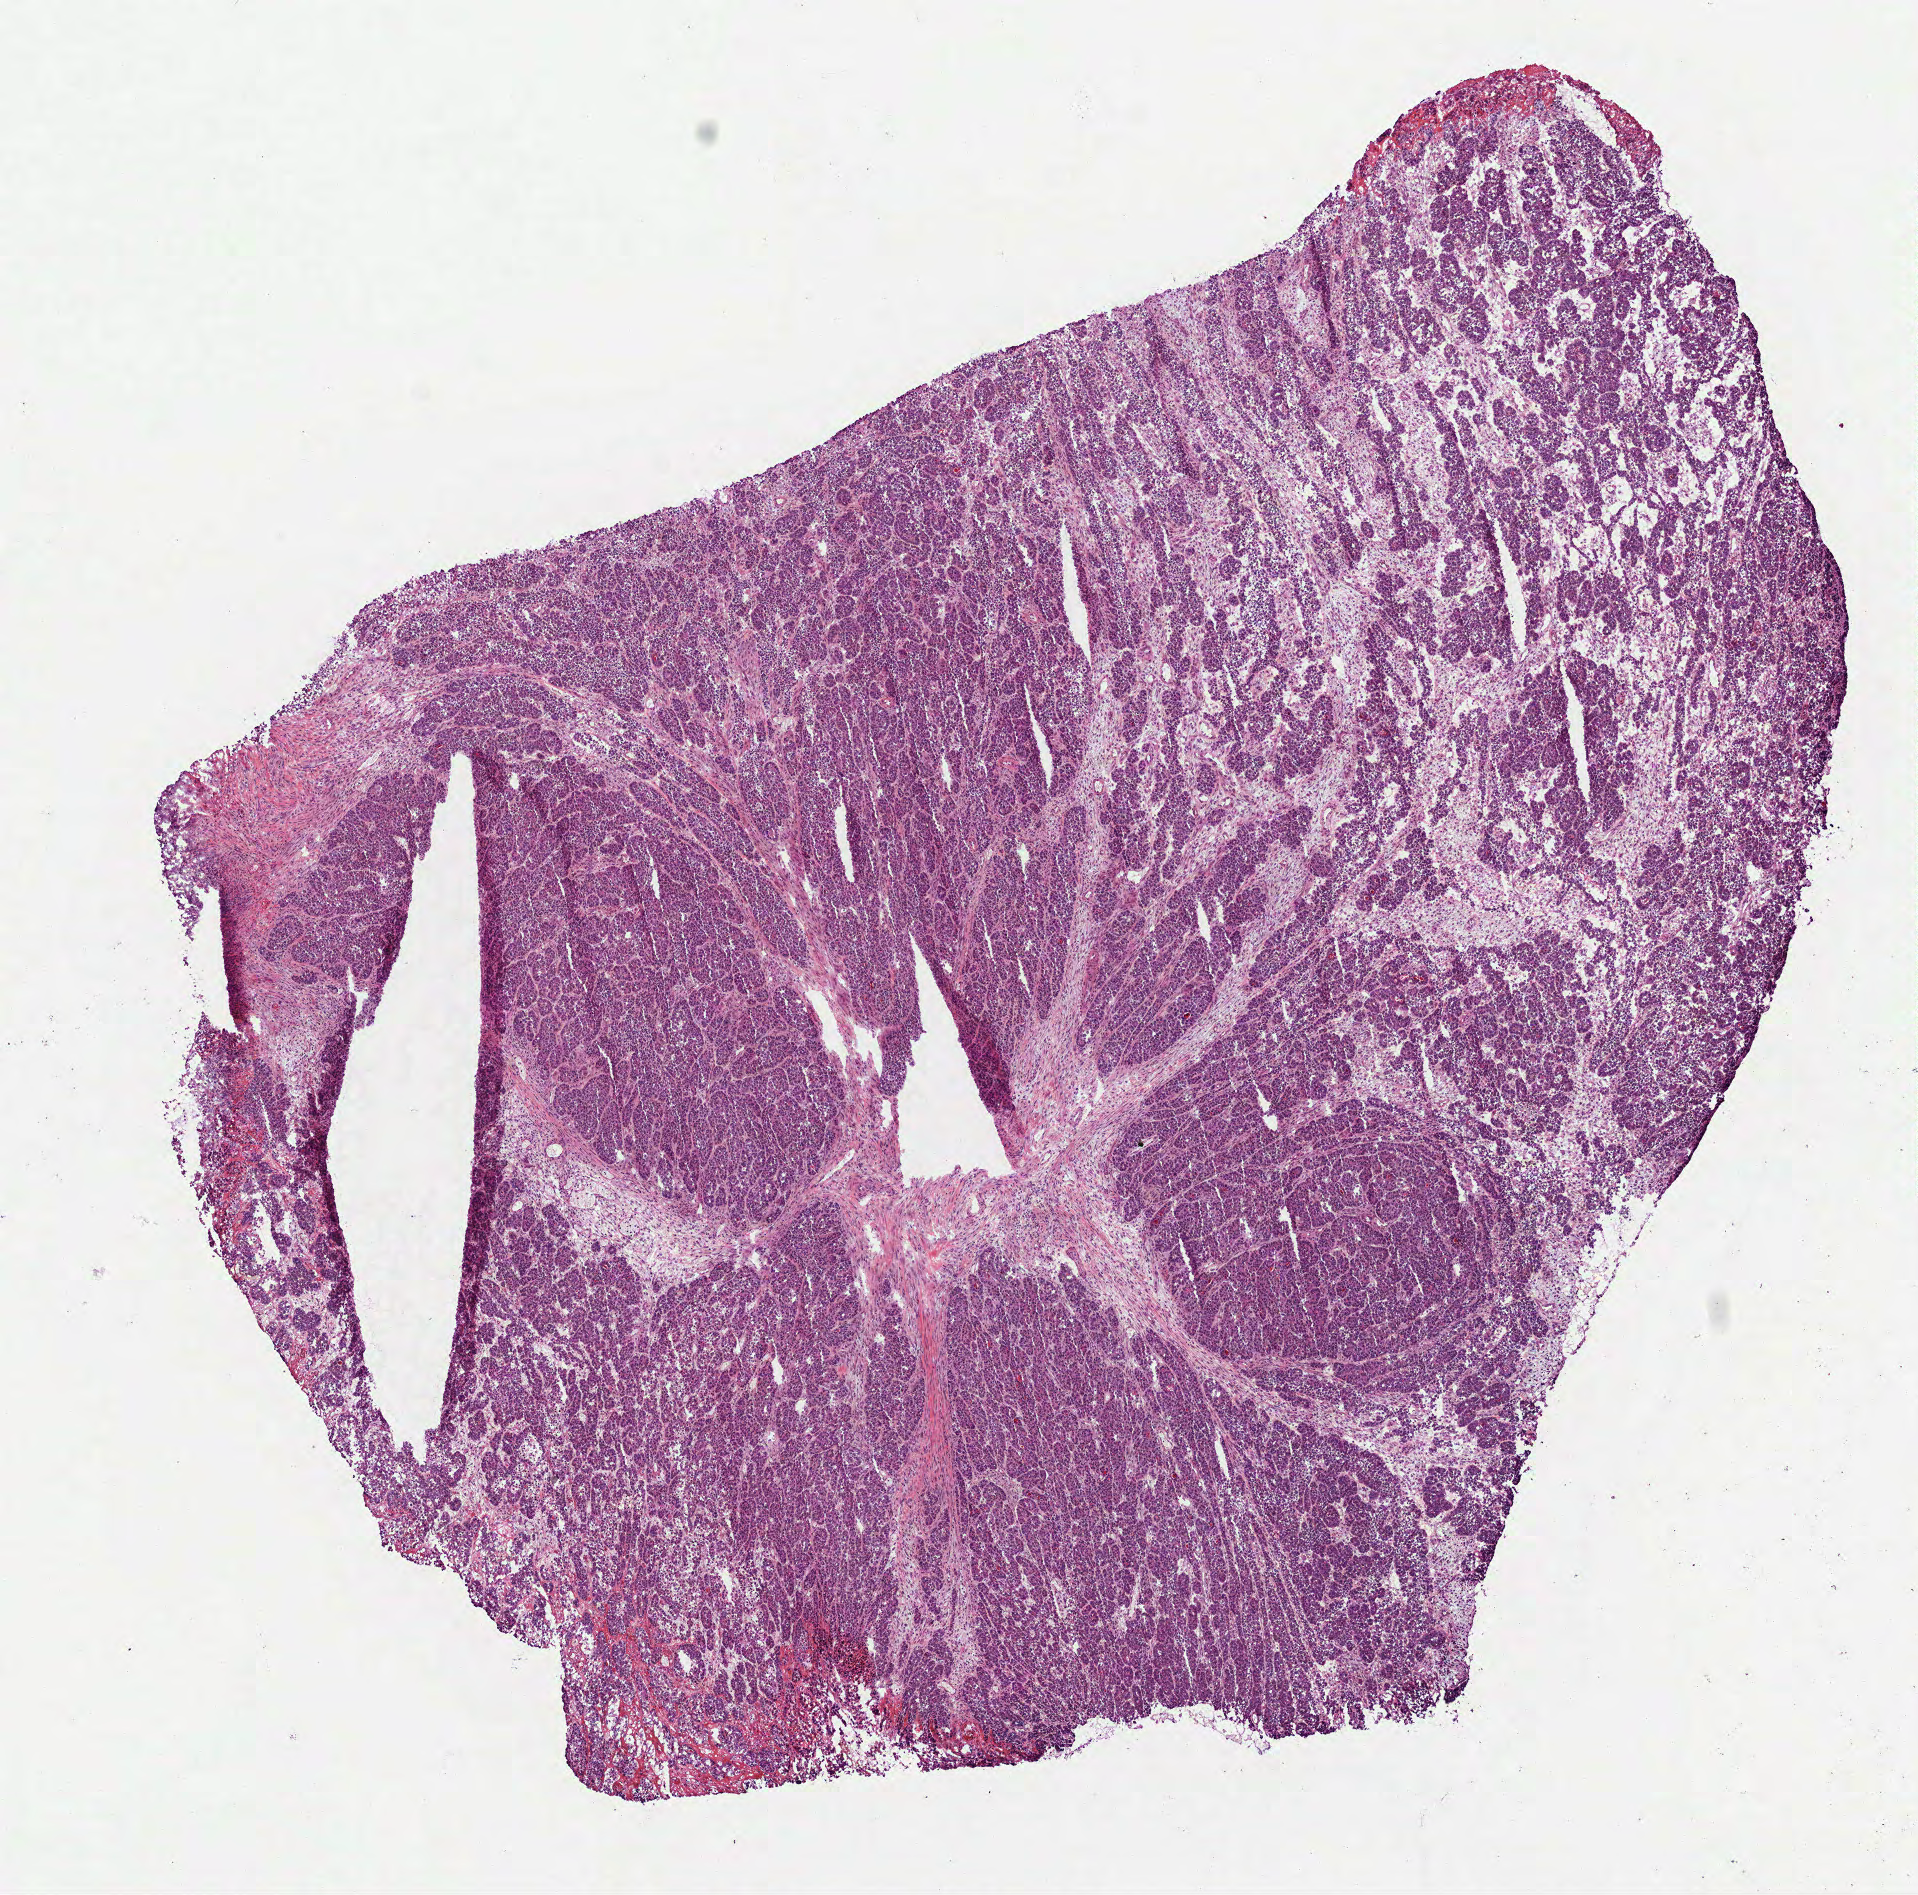
Digitized H&E-stained tissue section (whole slide) — whole scanned area (about 7.7 x 7.6 mm, acquisition: 40x scan) shown as a low-resolution overview. Frozen section. Stomach, primary tumour sample. Male, age 79 years at initial diagnosis. Histologic grade: G2 (moderately differentiated). Pathologist review of this section (percent, as recorded): tumour cells 100%, tumour nuclei 85%, normal cells 0%, stromal cells 0%, necrosis 0%. Infiltration values recorded for this section: lymphocyte infiltration 2%, monocyte infiltration 0%, neutrophil infiltration 0%.
- pathologic diagnosis: Adenocarcinoma, NOS
- lymph nodes positive (case pathology): 0 of 17 examined
- AJCC pathologic stage: IA (4th edition)